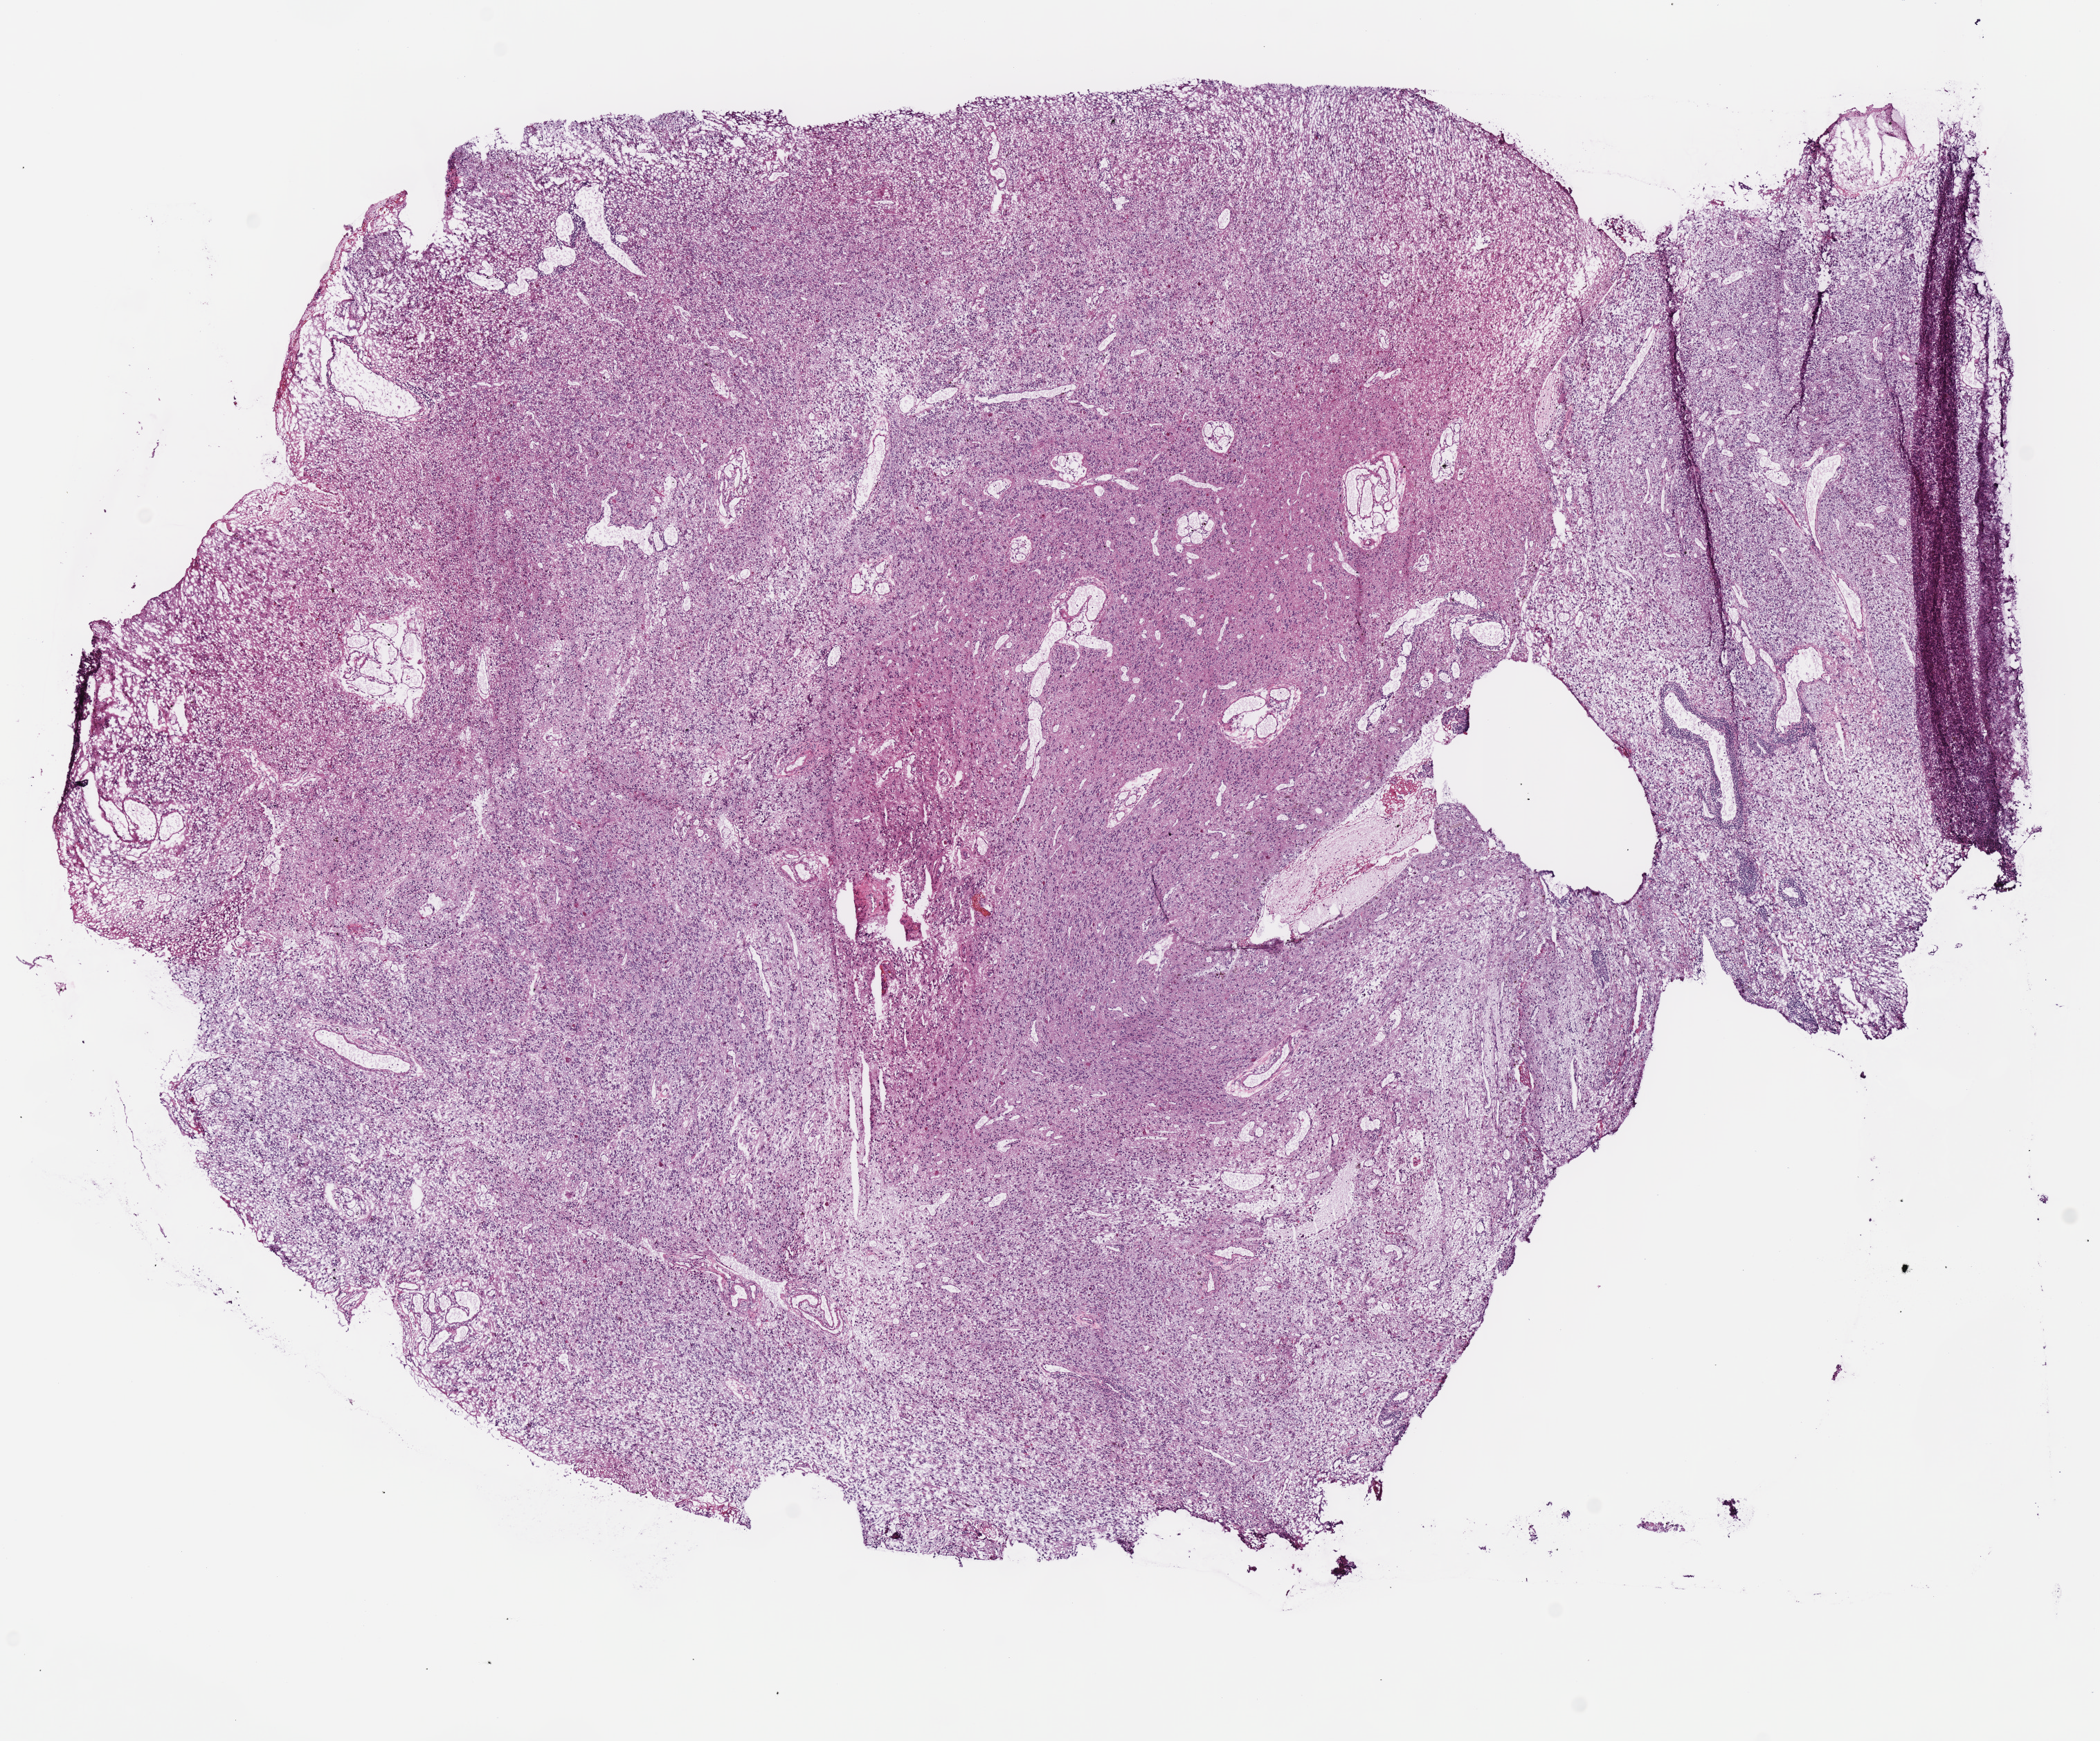
H&E-stained whole-slide image — a low-resolution overview of the entire scanned area, about 12.0 x 9.9 mm, frozen section, brain, primary tumour sample. Male, age 75 years at initial diagnosis. Histologic grade: G3 (poorly differentiated). Slide review estimates, as recorded: tumour cells 100%, tumour nuclei 85%, normal cells 0%, stromal cells 0%, necrosis 0%.
Laterality: right. Pathologic diagnosis: Oligodendroglioma, anaplastic.